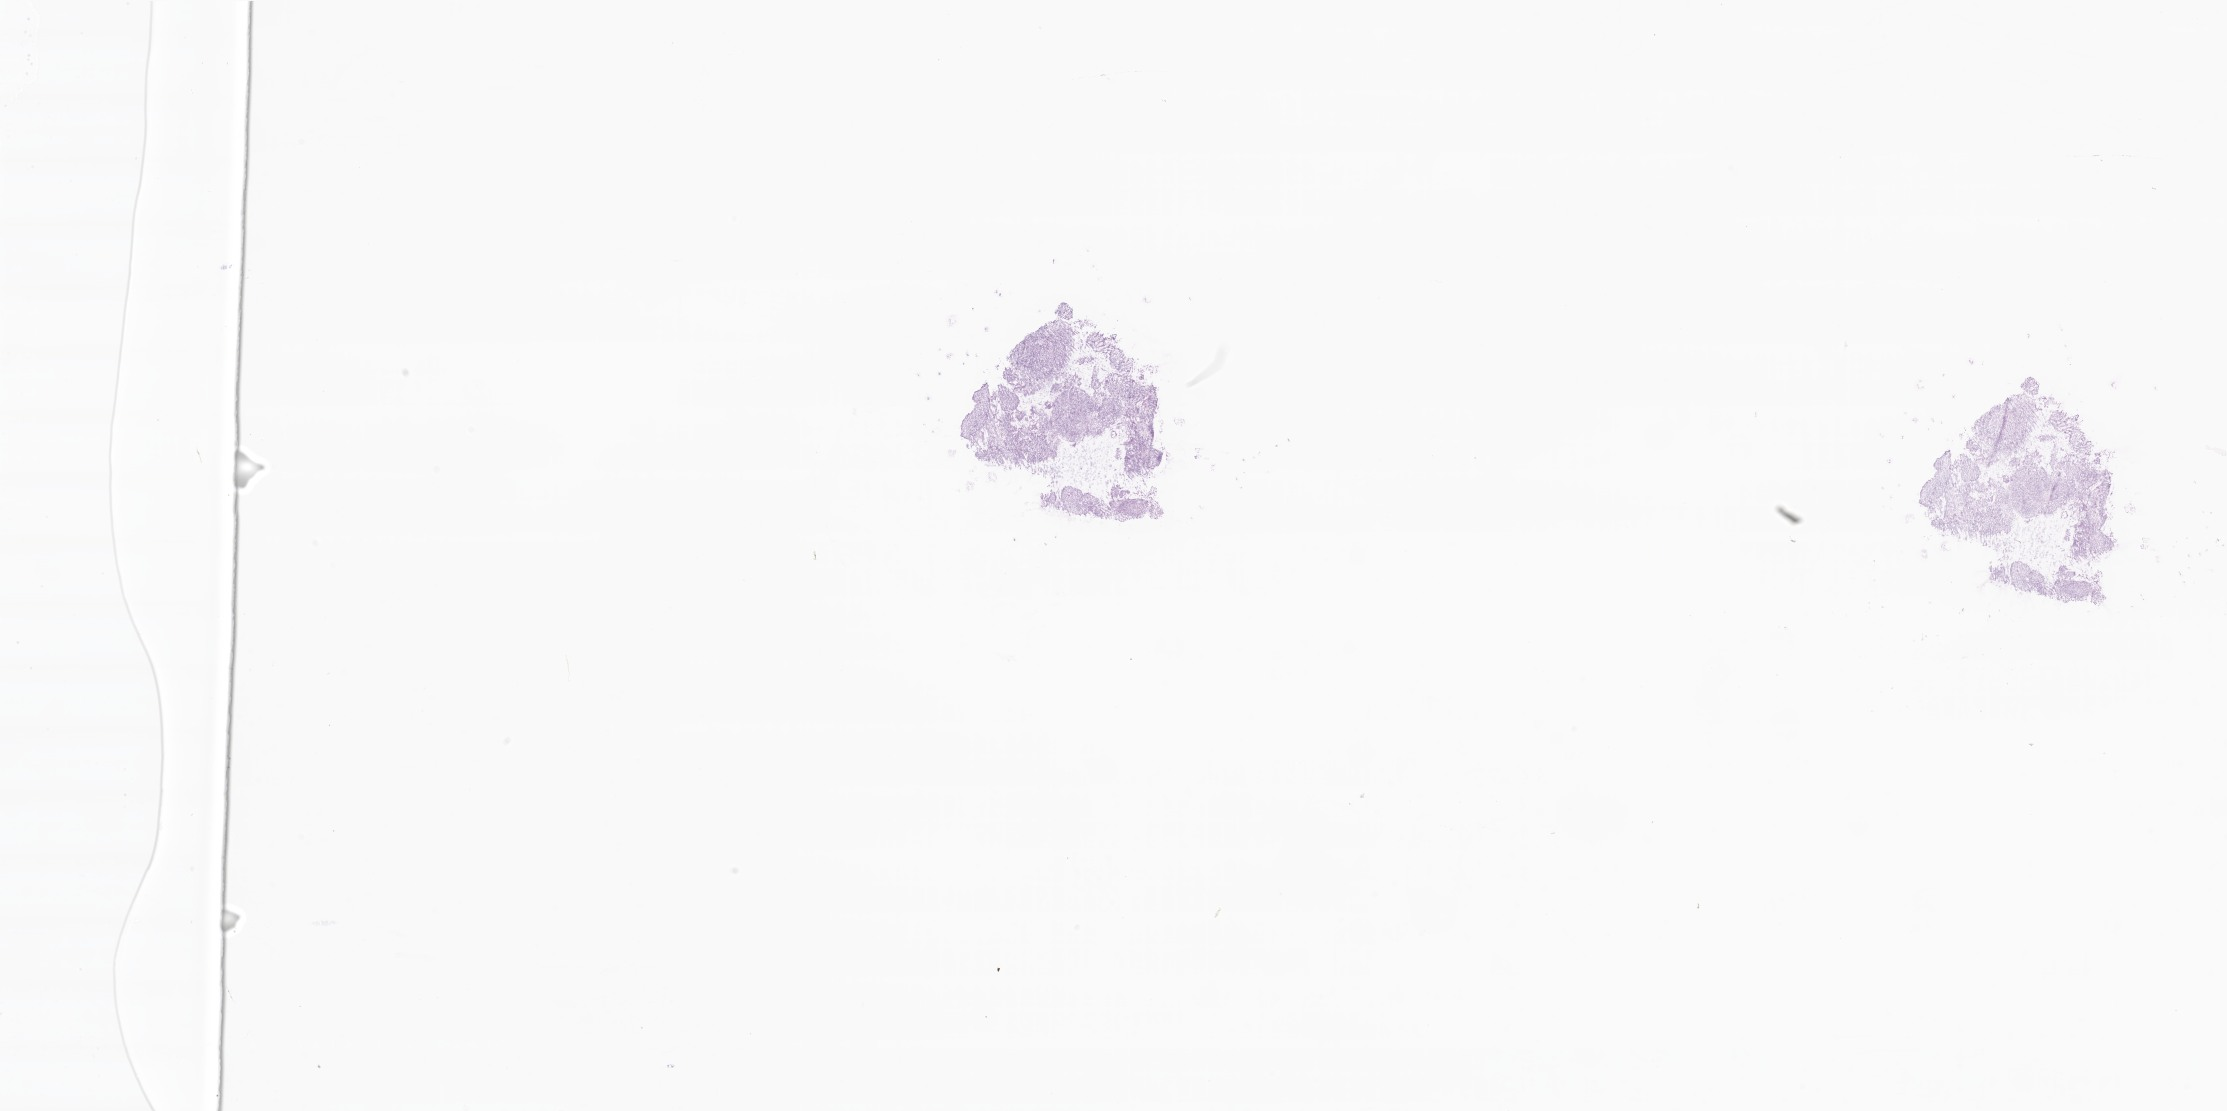
Whole-slide image, haematoxylin and eosin stain, low-resolution overview of the scanned area, about 37.6 x 18.7 mm. Frozen section (tissue freezing medium). Specimen: primary tumor. Site: lower lobe of left lung. Male, age 82 years at initial diagnosis. Composition of this section per pathologist review: tumor cells 60%, tumor nuclei 60%, stromal cells 40%, necrosis 0%, normal cells 0%. Infiltration values recorded for this section: lymphocyte infiltration 100%, monocyte infiltration 0%, neutrophil infiltration 0%.
- histologic diagnosis: Squamous cell carcinoma, NOS
- section: top of the tissue portion